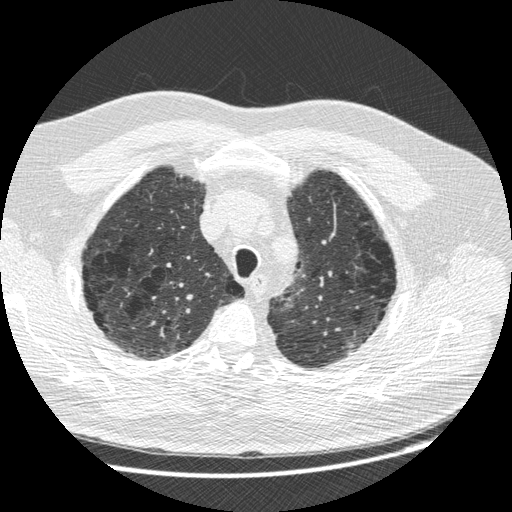
Low-dose screening chest CT, one axial slice. Position 209 of 258 along the scan axis. 120 kVp. Lung window (W 1500 / L -600 HU). 1.25 mm slice thickness. 512 × 512 image matrix.
Annotated regions visible in this slice (expert manual segmentation):
- lesion 1 (tumor, upper lobe of left lung): bounding box <348,343,354,349> (left, top, right, bottom; pixels)